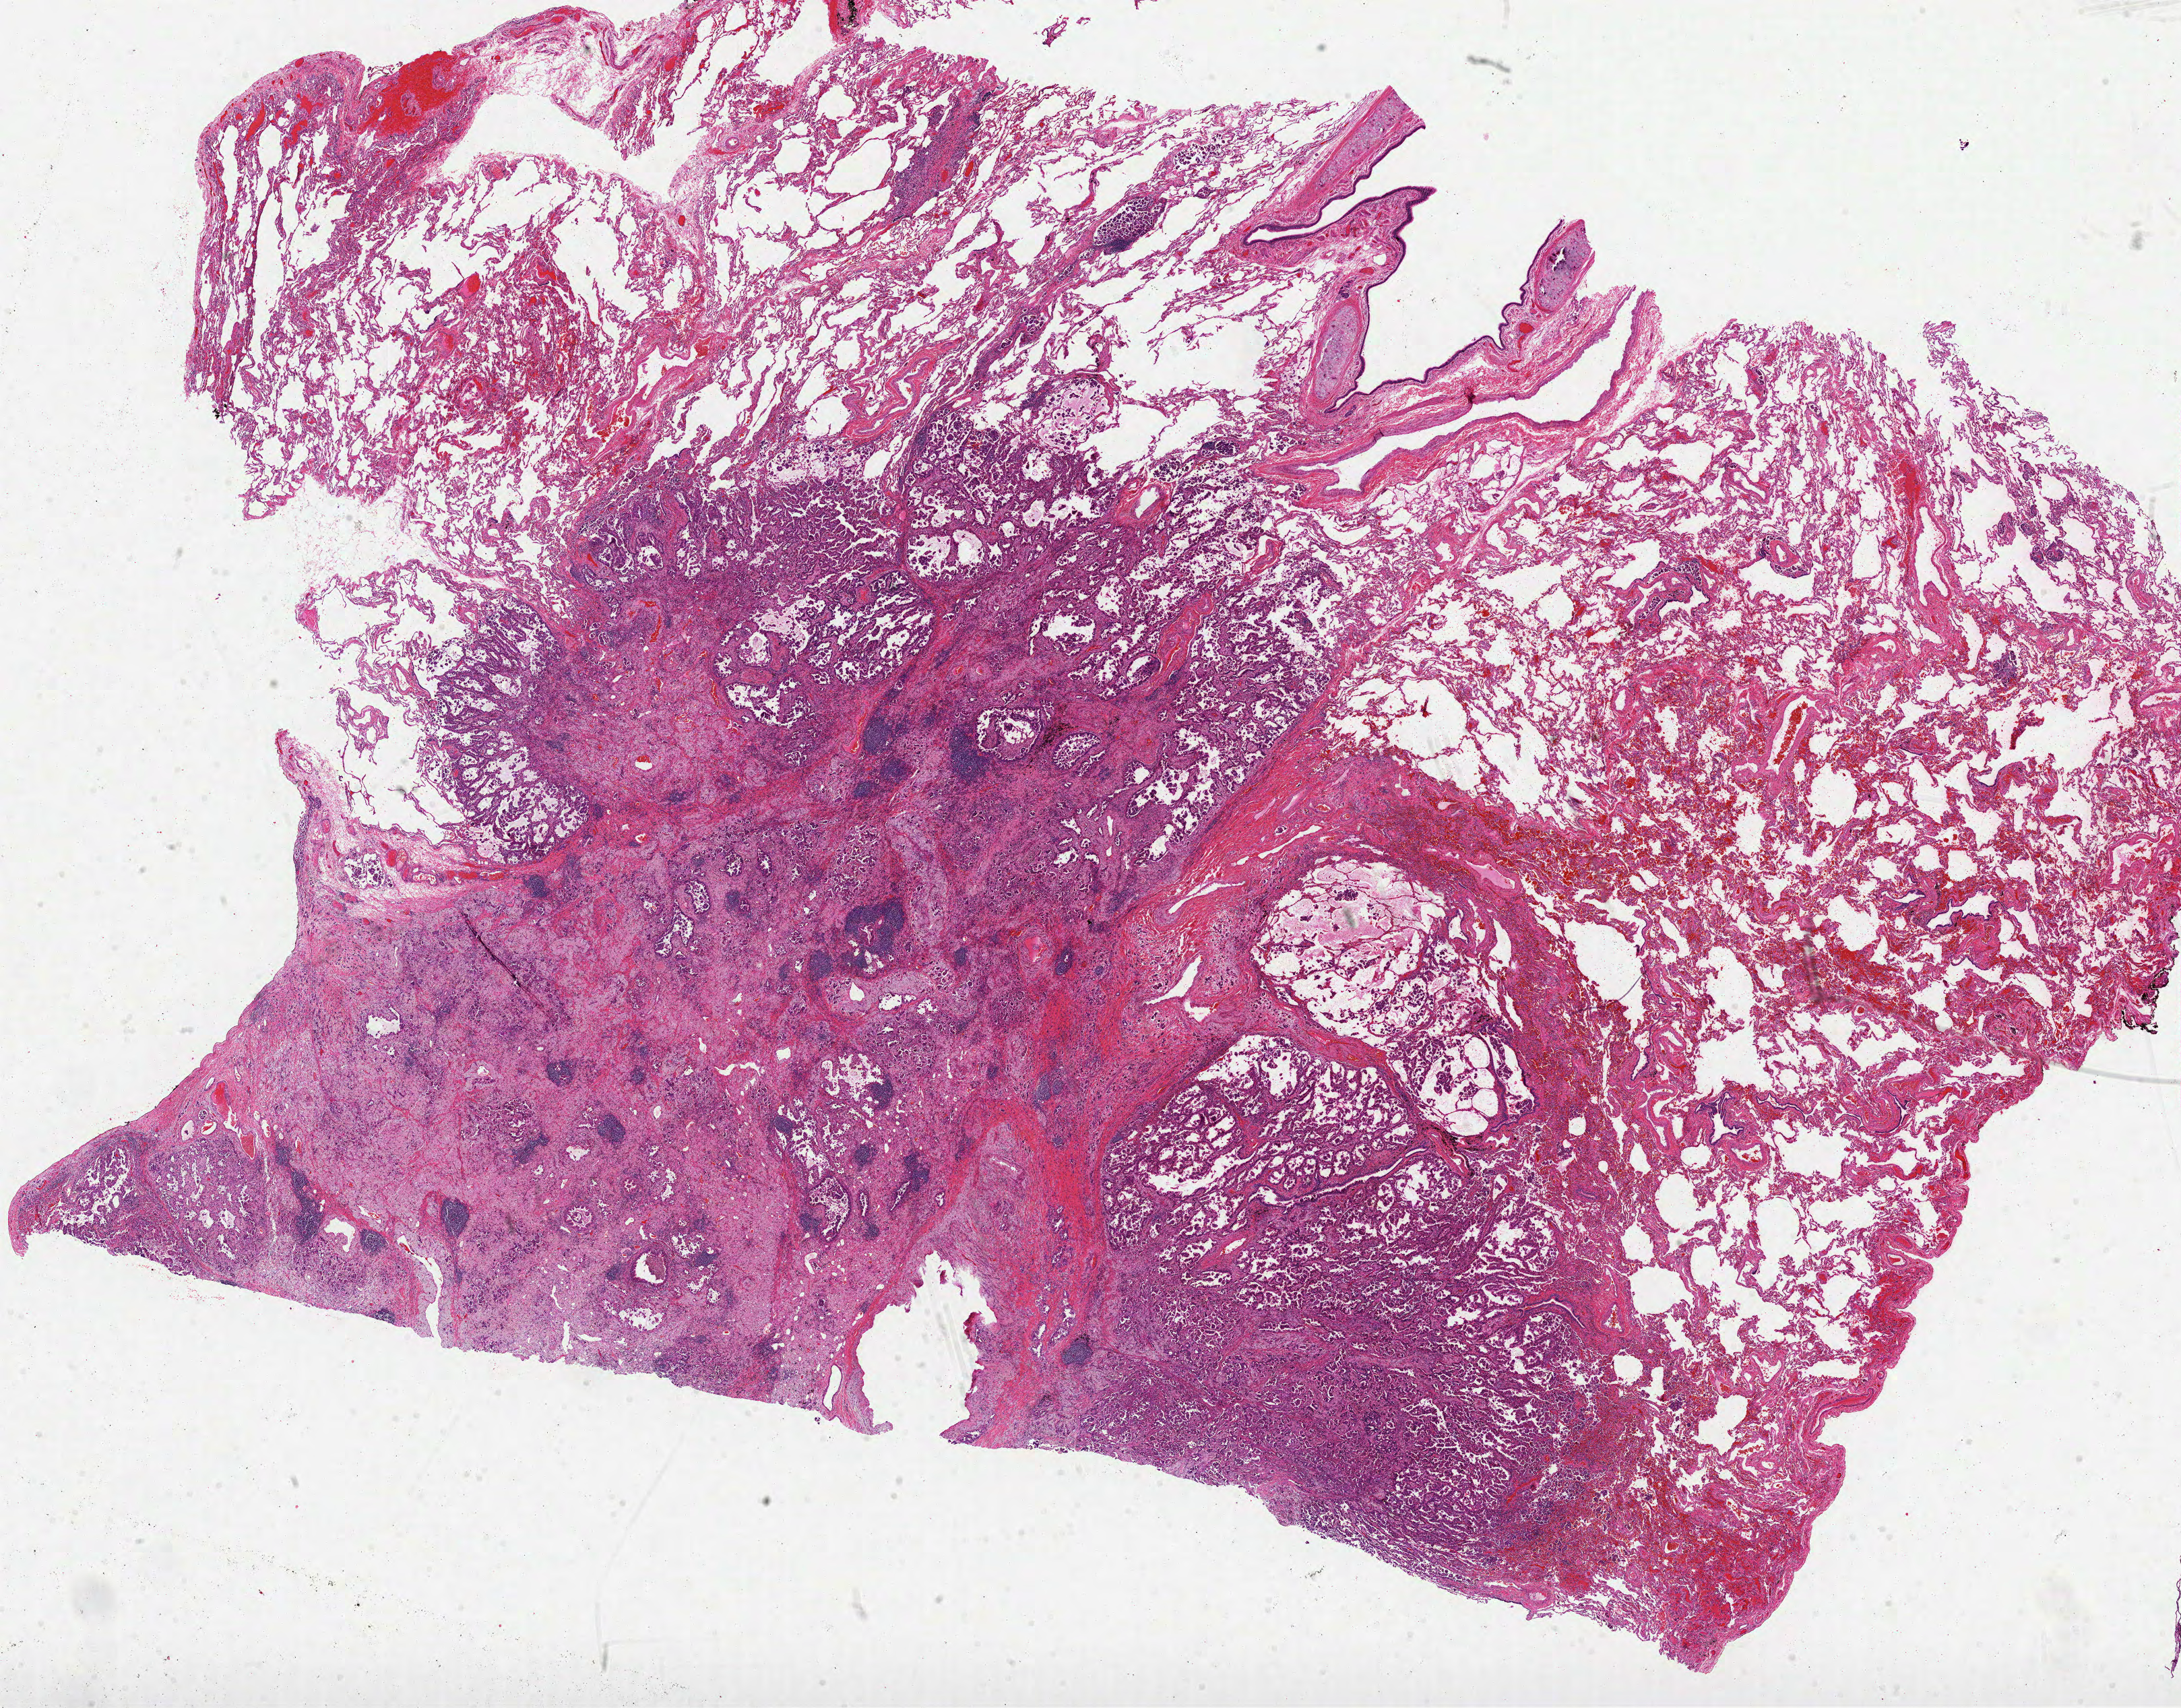
Whole-slide histology image, Hematoxylin and eosin (H&E) stained, whole scanned area (about 26.1 x 20.4 mm) shown as a low-resolution overview; formalin-fixed paraffin-embedded (FFPE) diagnostic section; sample: primary tumour, lung. Patient: female, age at initial diagnosis 69 years.
• histologic diagnosis: Adenocarcinoma, NOS (middle lobe, lung)
• laterality: right
• AJCC pathologic stage: IIIA (6th edition)